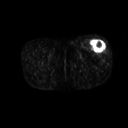
FDG PET of an extremity soft-tissue mass (from a PET/CT study), one axial slice; position 227 of 267 along the scan axis; 3.27 mm slice thickness; 128 × 128 image matrix, field of view 500 × 500 mm. Patient: male, 64 years. From the clinical record (not read from this slice): histological type: extraskeletal osteosarcoma; grade: high; site of the primary tumour: thigh.
Outlined on this slice (expert contour drawn on MRI and transferred to this co-registered scan by the dataset authors):
- gross tumour volume (mass): bounding box [x1, y1, x2, y2] px = [91, 40, 106, 52]